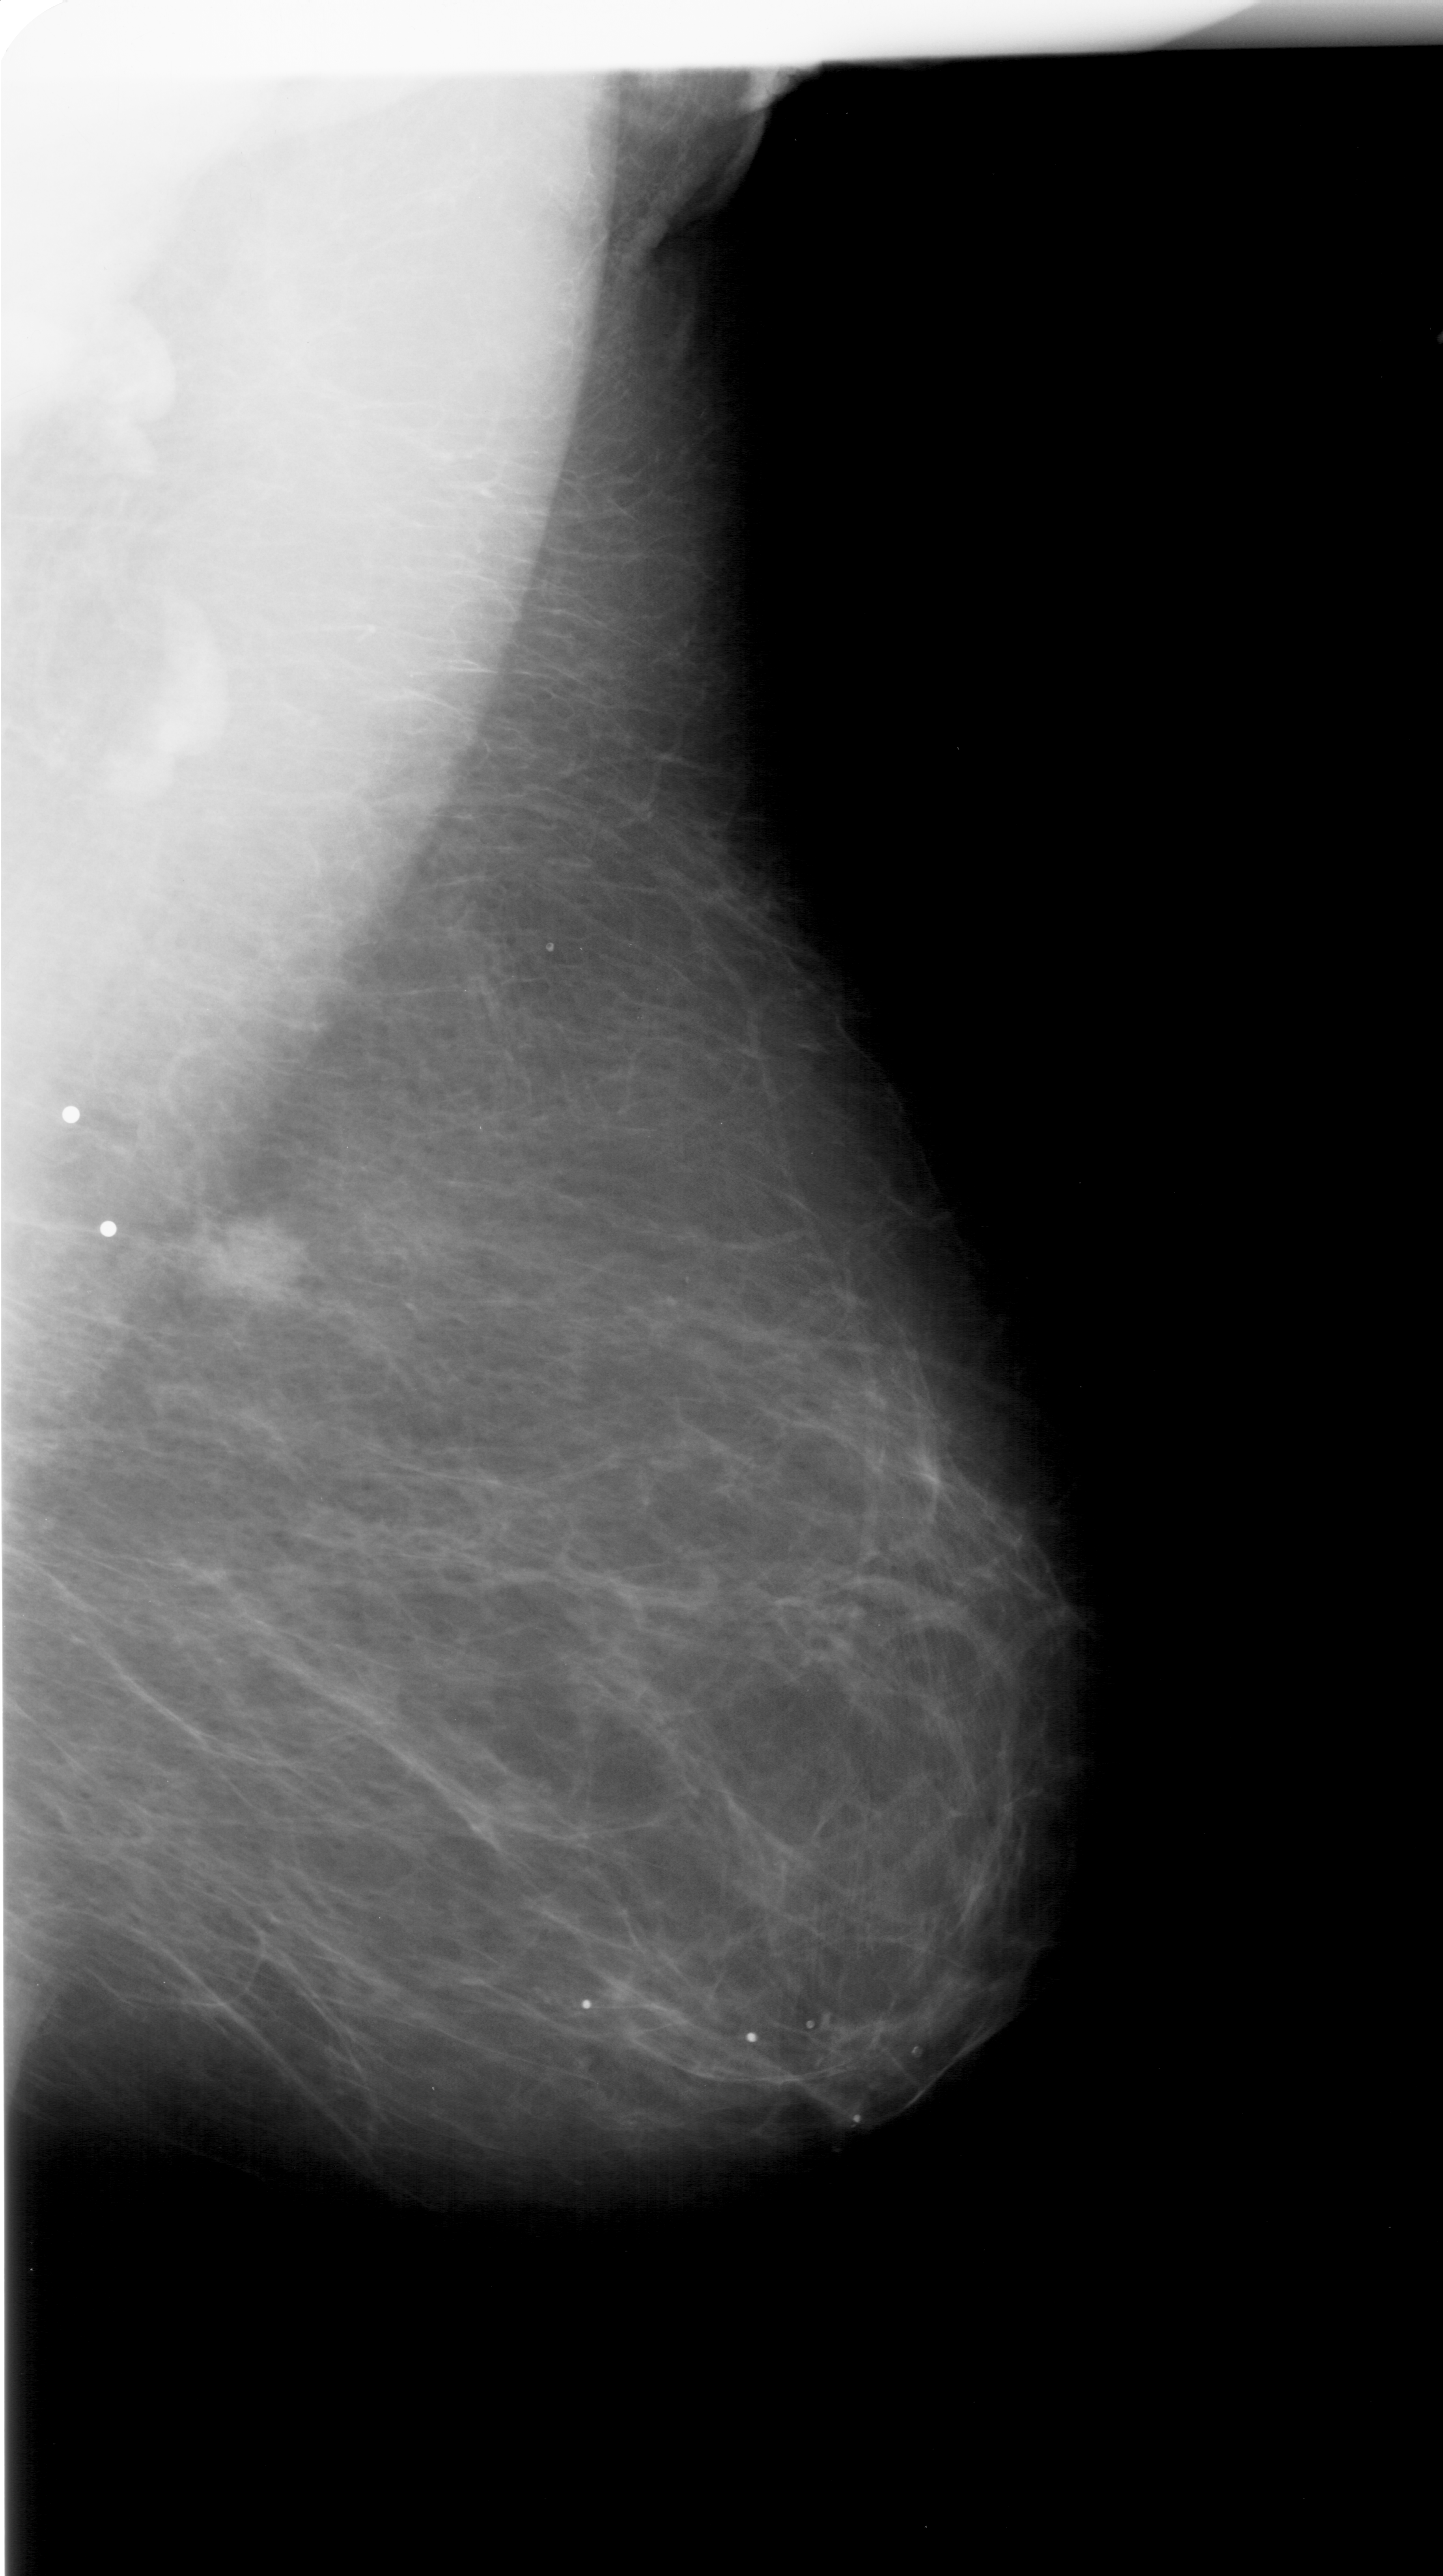
Mammogram (digitized film); right breast; MLO view; breast composition: almost entirely fatty (BI-RADS density category 1 of 4).
- Radiologist-marked abnormalities on this image: mass, shape irregular, margins ill defined; BI-RADS assessment category 5; subtlety rating 5 on a 1 (subtle) to 5 (obvious) scale; pathology (as recorded): malignant.